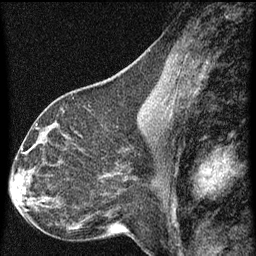
Breast MRI (dynamic contrast-enhanced), one sagittal slice; slice 33 of 60 in the series (ordered by position); dynamic contrast-enhanced series, image 2 of 3 at this slice position (ordered by acquisition); 1.5 T; TE 4.2 ms, TR 8 ms; 2 mm slice thickness; 256 × 256 image matrix, field of view 180 × 180 mm. Patient: female, 44 years.
Structures marked on this image (semi-automatic segmentation, software-assisted and operator-edited):
- analysis volume of interest (the breast-tissue region the enhancement analysis was run in; not a lesion): box from (x=49, y=128) to (x=95, y=169) px
- tumour enhancement mask (voxels above the 70 % enhancement threshold inside the analysis volume of interest): (x=63, y=134)–(x=67, y=137)